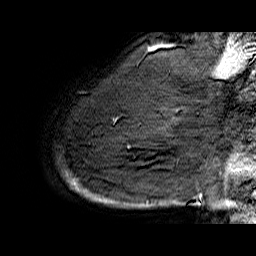
Breast MRI (dynamic contrast-enhanced), one sagittal slice; position 51 of 60 along the scan axis; dynamic contrast-enhanced series, time point 2 of 6 at this slice position (early post-contrast); 1.5 T; TE 6.4 ms, TR 32.9 ms; 4 mm slice thickness; 256 × 256 image matrix, field of view 200 × 200 mm. Female patient. Case-level facts recorded for this patient, not image findings: setting: breast cancer imaged before/during neoadjuvant chemotherapy; receptor status: HR-positive, HER2-negative.
Structures marked on this image (semi-automatically segmented with operator editing):
- analysis volume of interest (the breast-tissue region the enhancement analysis was run in; not a lesion): bounding box (x1, y1, x2, y2) in pixels: (61, 74, 176, 209)
- tumour enhancement mask (voxels above the 100 % enhancement threshold inside the analysis volume of interest): (73, 178, 78, 190)